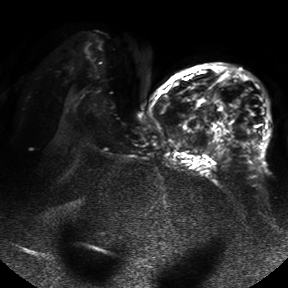
Breast MRI, one axial slice. Position 24 of 50 along the scan axis. Diffusion-weighted series; image 2 of 4 stored at this slice position (different b-values; order by instance number). 1.5 T. 288 × 288 image matrix, field of view 390 × 390 mm. Female patient.
Outlined on this slice (manually delineated by an expert):
- tumour on diffusion-weighted imaging: box from (x=230, y=99) to (x=244, y=135) px